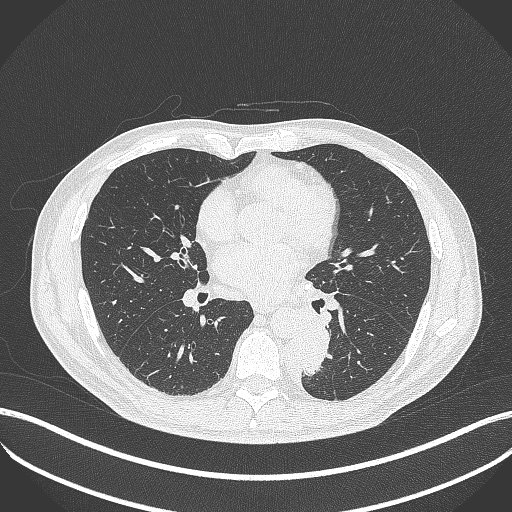
Chest CT, one axial slice; slice 198 of 451 in the series (ordered by position); reconstruction kernel B70f; lung window (W 1500 / L -600 HU); 1 mm slice thickness; 512 × 512 image matrix. Male patient, age 72 years. From the clinical record (not read from this slice): clinical TNM (as recorded): T2b N0 M1.
Annotated regions visible in this slice (bounding box drawn by a radiologist):
- lung tumour (recorded histology: adenocarcinoma): bounding box (x1, y1, x2, y2) in pixels: (299, 320, 331, 379)